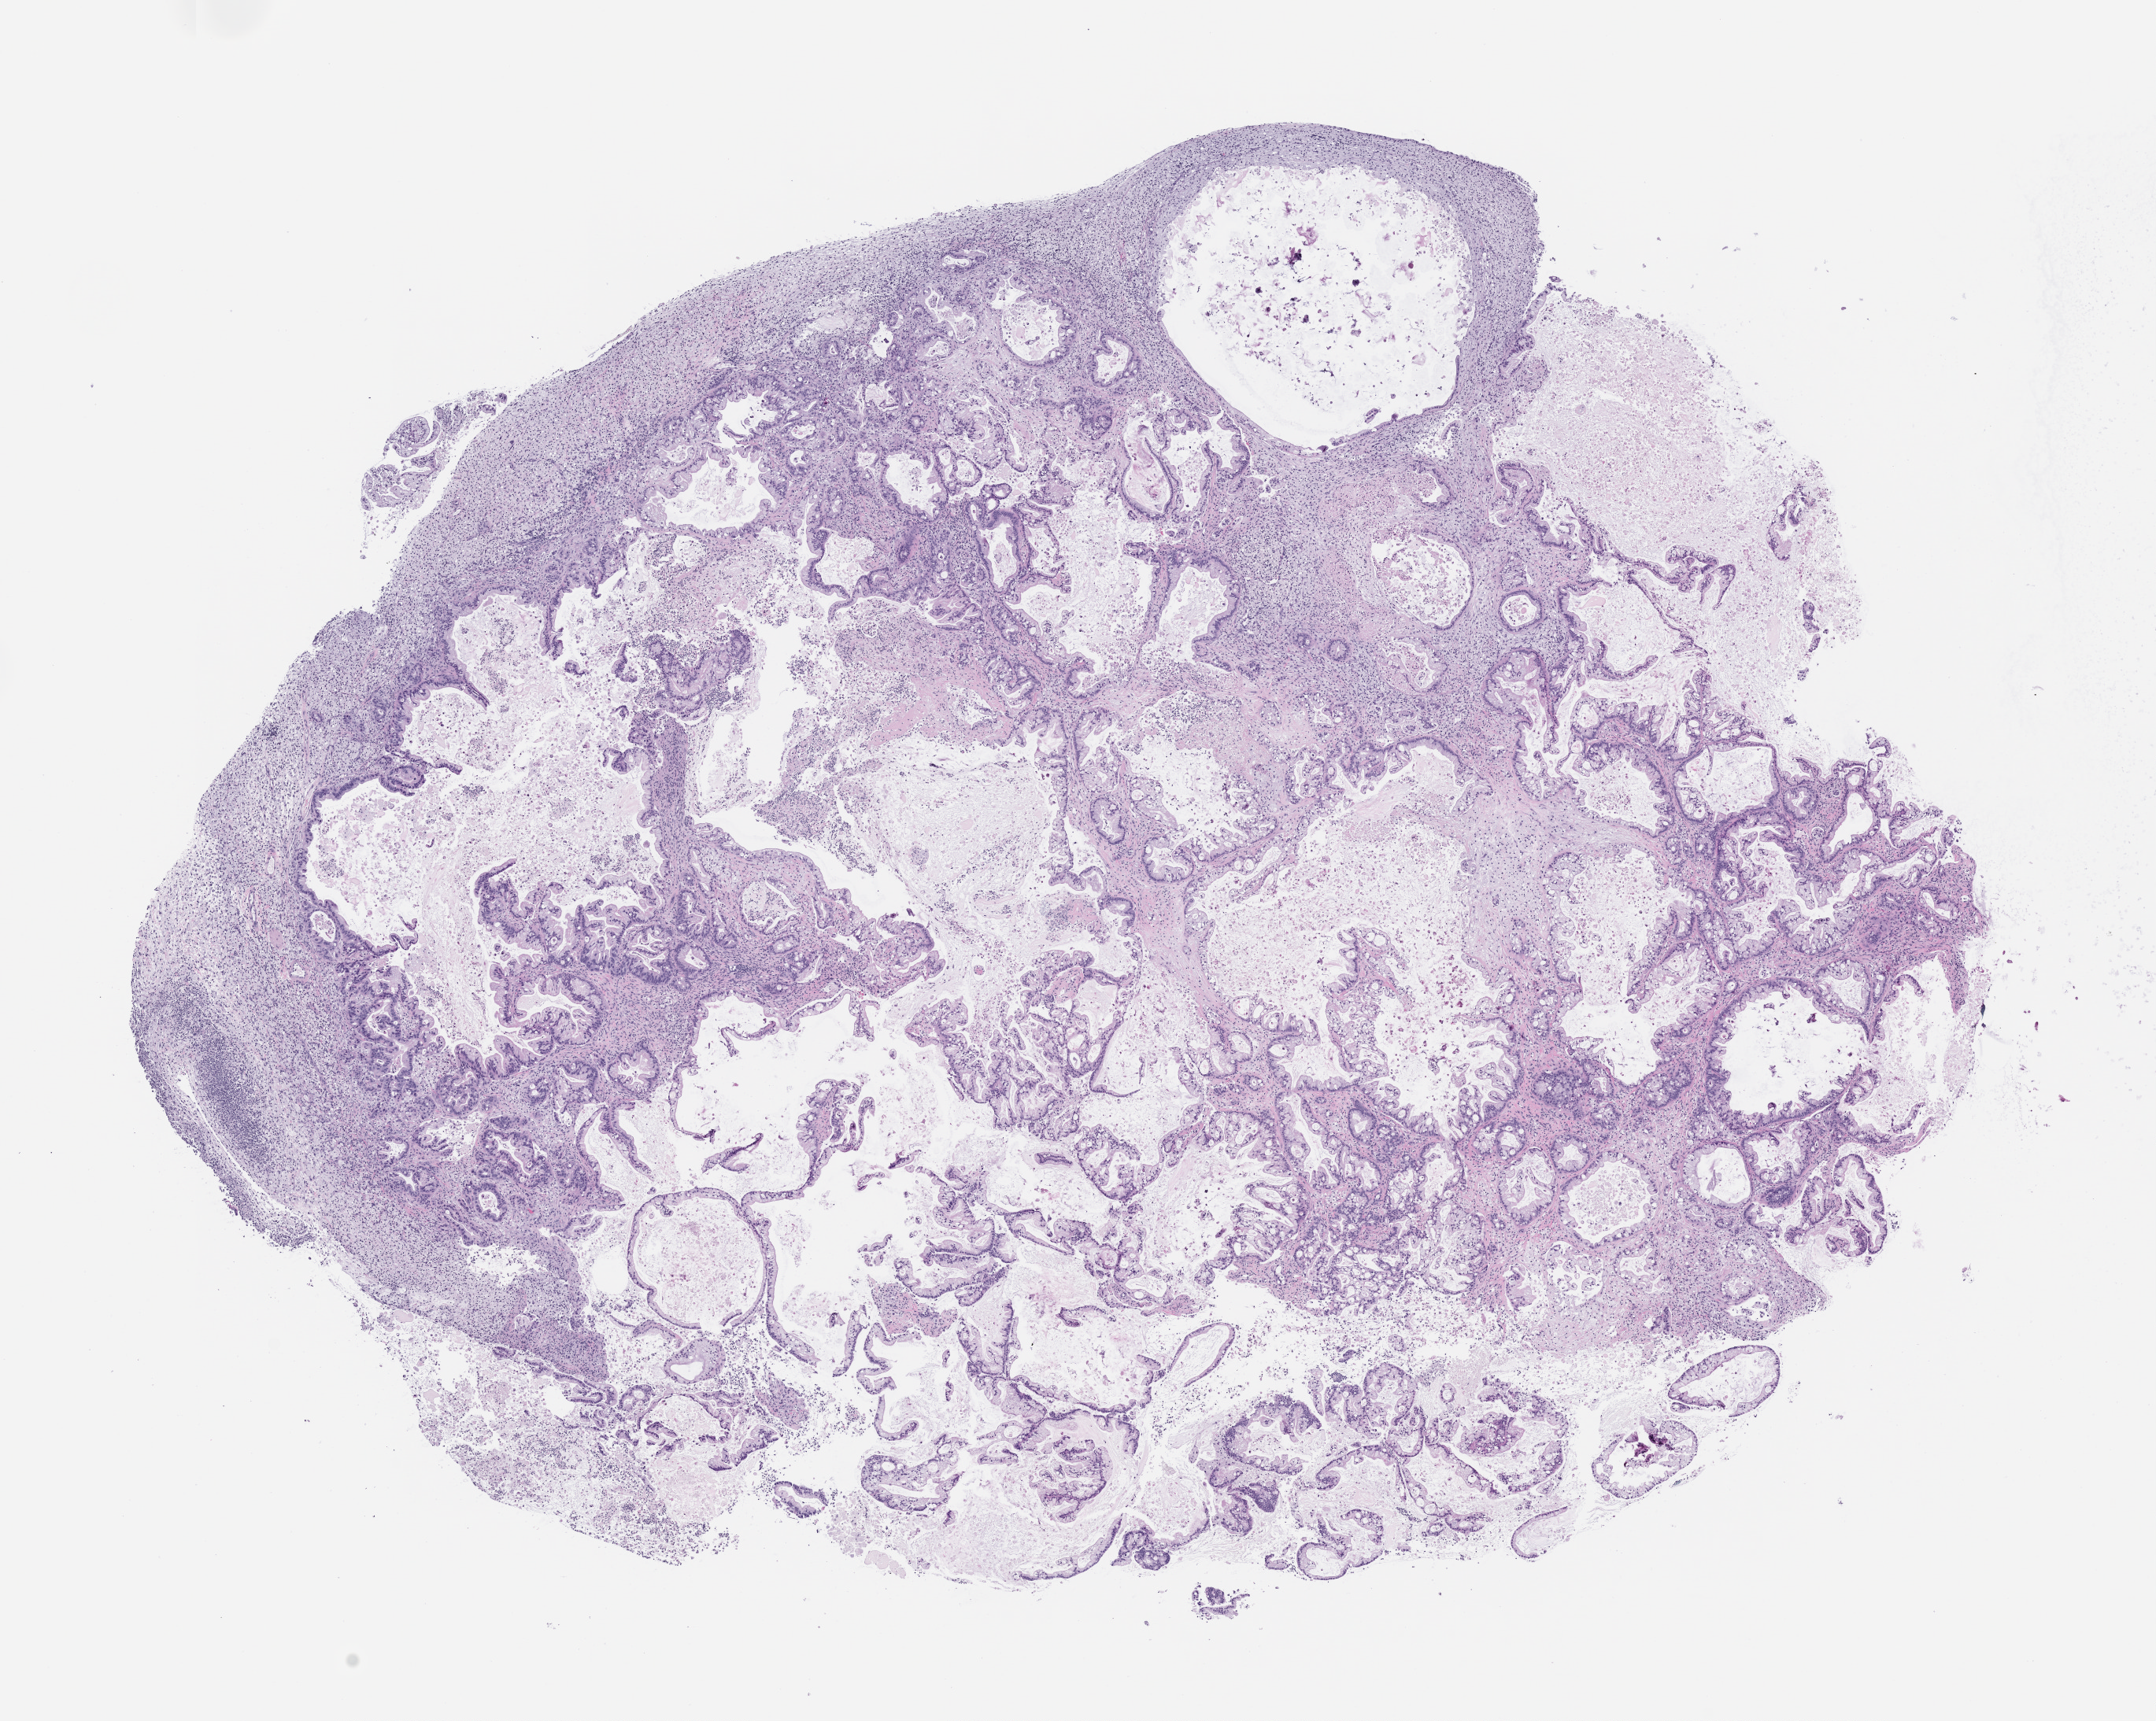
Haematoxylin and eosin whole-slide image of a patient-derived xenograft (PDX) tumor grown in a mouse, passage 1 — whole scanned area (about 11.0 x 8.8 mm) shown as a low-resolution overview, FFPE section, tumor site category: pancreas.
Originating patient diagnosis: Pancreatic Adenocarcinoma.